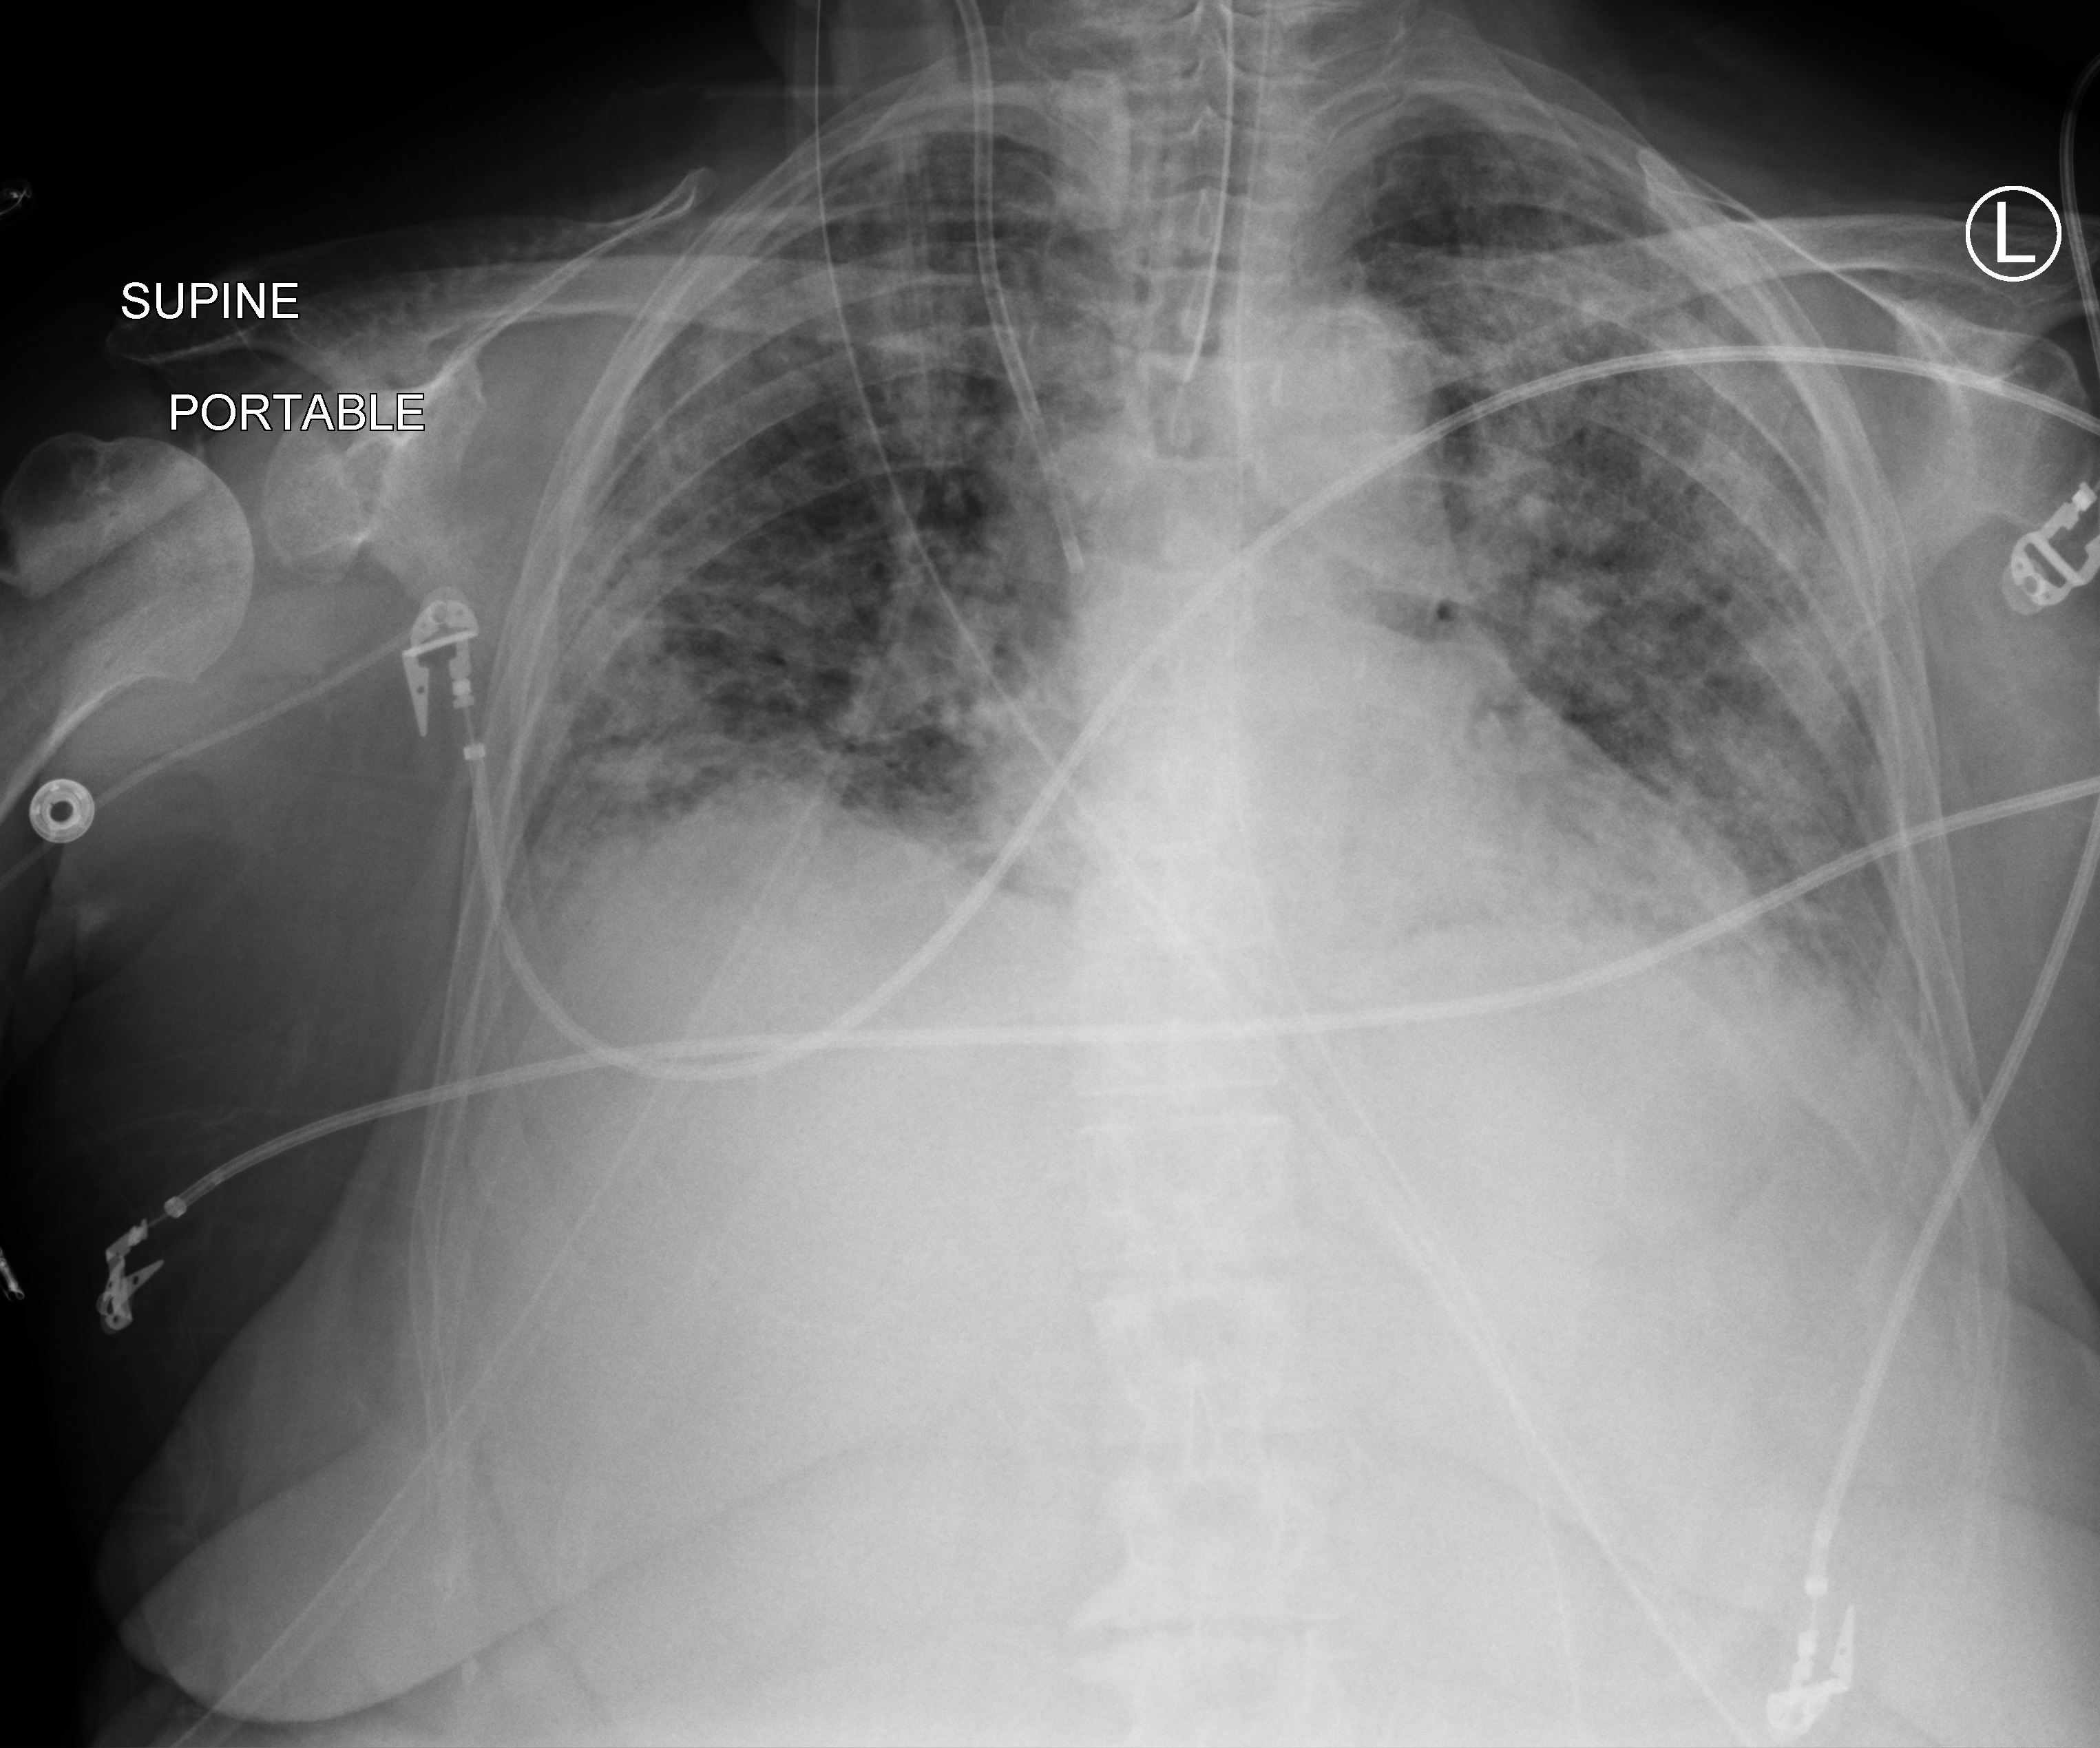
Portable chest radiograph, anteroposterior (AP) projection. Female patient hospitalised with COVID-19, age 75–90 years.
Hospital-stay facts (about this admission, not read from this image; timing relative to this image not recorded):
- admitted to intensive care during this hospital stay: yes
- smoking status (admission record): former
- mechanically ventilated during this hospital stay: yes